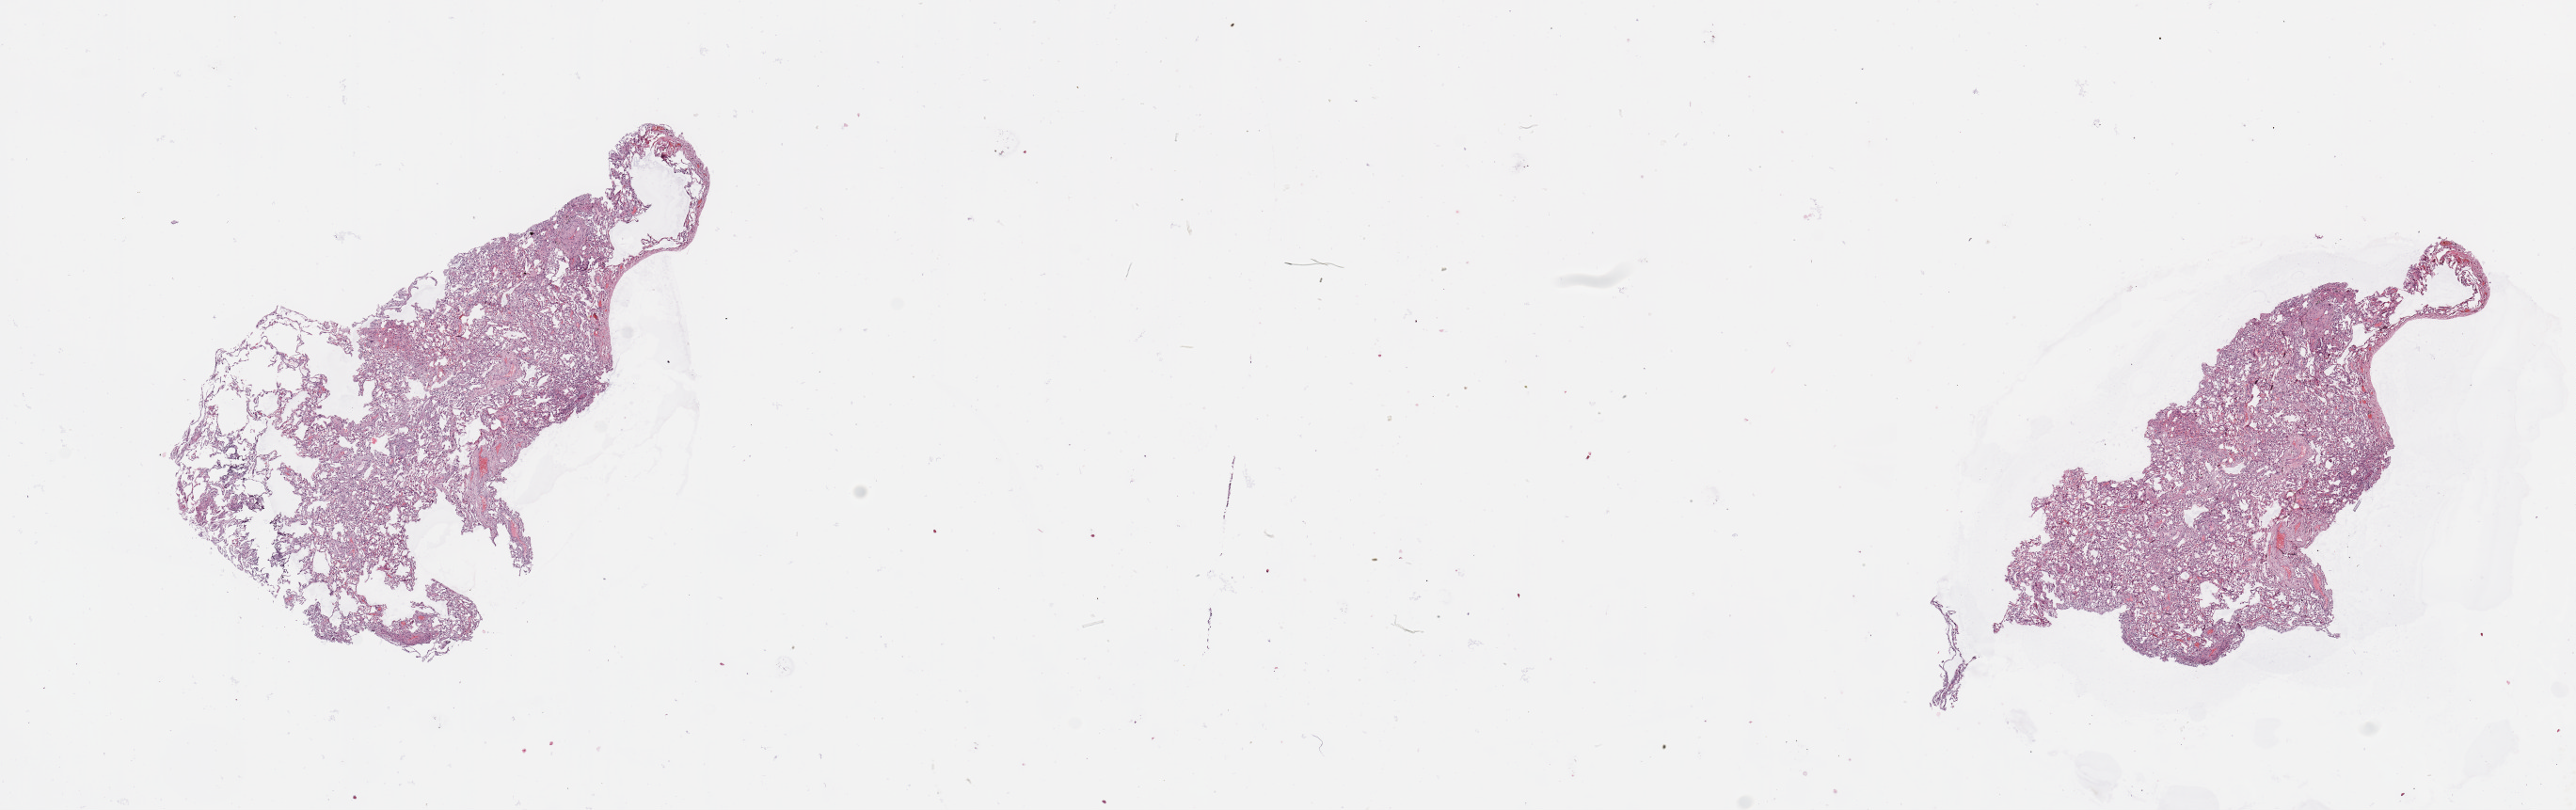
H&E whole-slide image, whole scanned area (about 21.7 x 6.8 mm) shown as a low-resolution overview. Normal (non-tumour) tissue sample, sampled site: lung. Patient: female, age 70 years.
* this section: normal (non-tumour) tissue from the same patient
* patient diagnosis: Adenocarcinoma, NOS